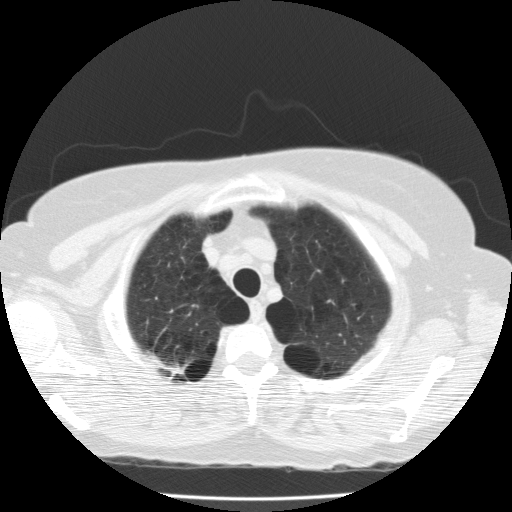
Chest CT (low-dose screening protocol), one axial image. Second screening round (one year after baseline). Lung window (W 1500 / L -600 HU). 2 mm slice thickness. Standard (soft-tissue) reconstruction kernel (FC10). 120 kVp. Slice 24 of 174 in the series. 512 × 512 image matrix. Female participant, aged 59 years at enrolment. Current smoker at enrolment.
• Expert-annotated lung lesion, bounding box [x1, y1, x2, y2] px = [139, 345, 195, 391].
• Screening reader's record for this exam (one nodule recorded; not confirmed to be the boxed lesion): non-calcified nodule or mass ≥4 mm, right upper lobe, 11 × 6 mm, spiculated (stellate) margins, soft tissue attenuation, pre-existing on the prior screen: yes; interval growth: no.